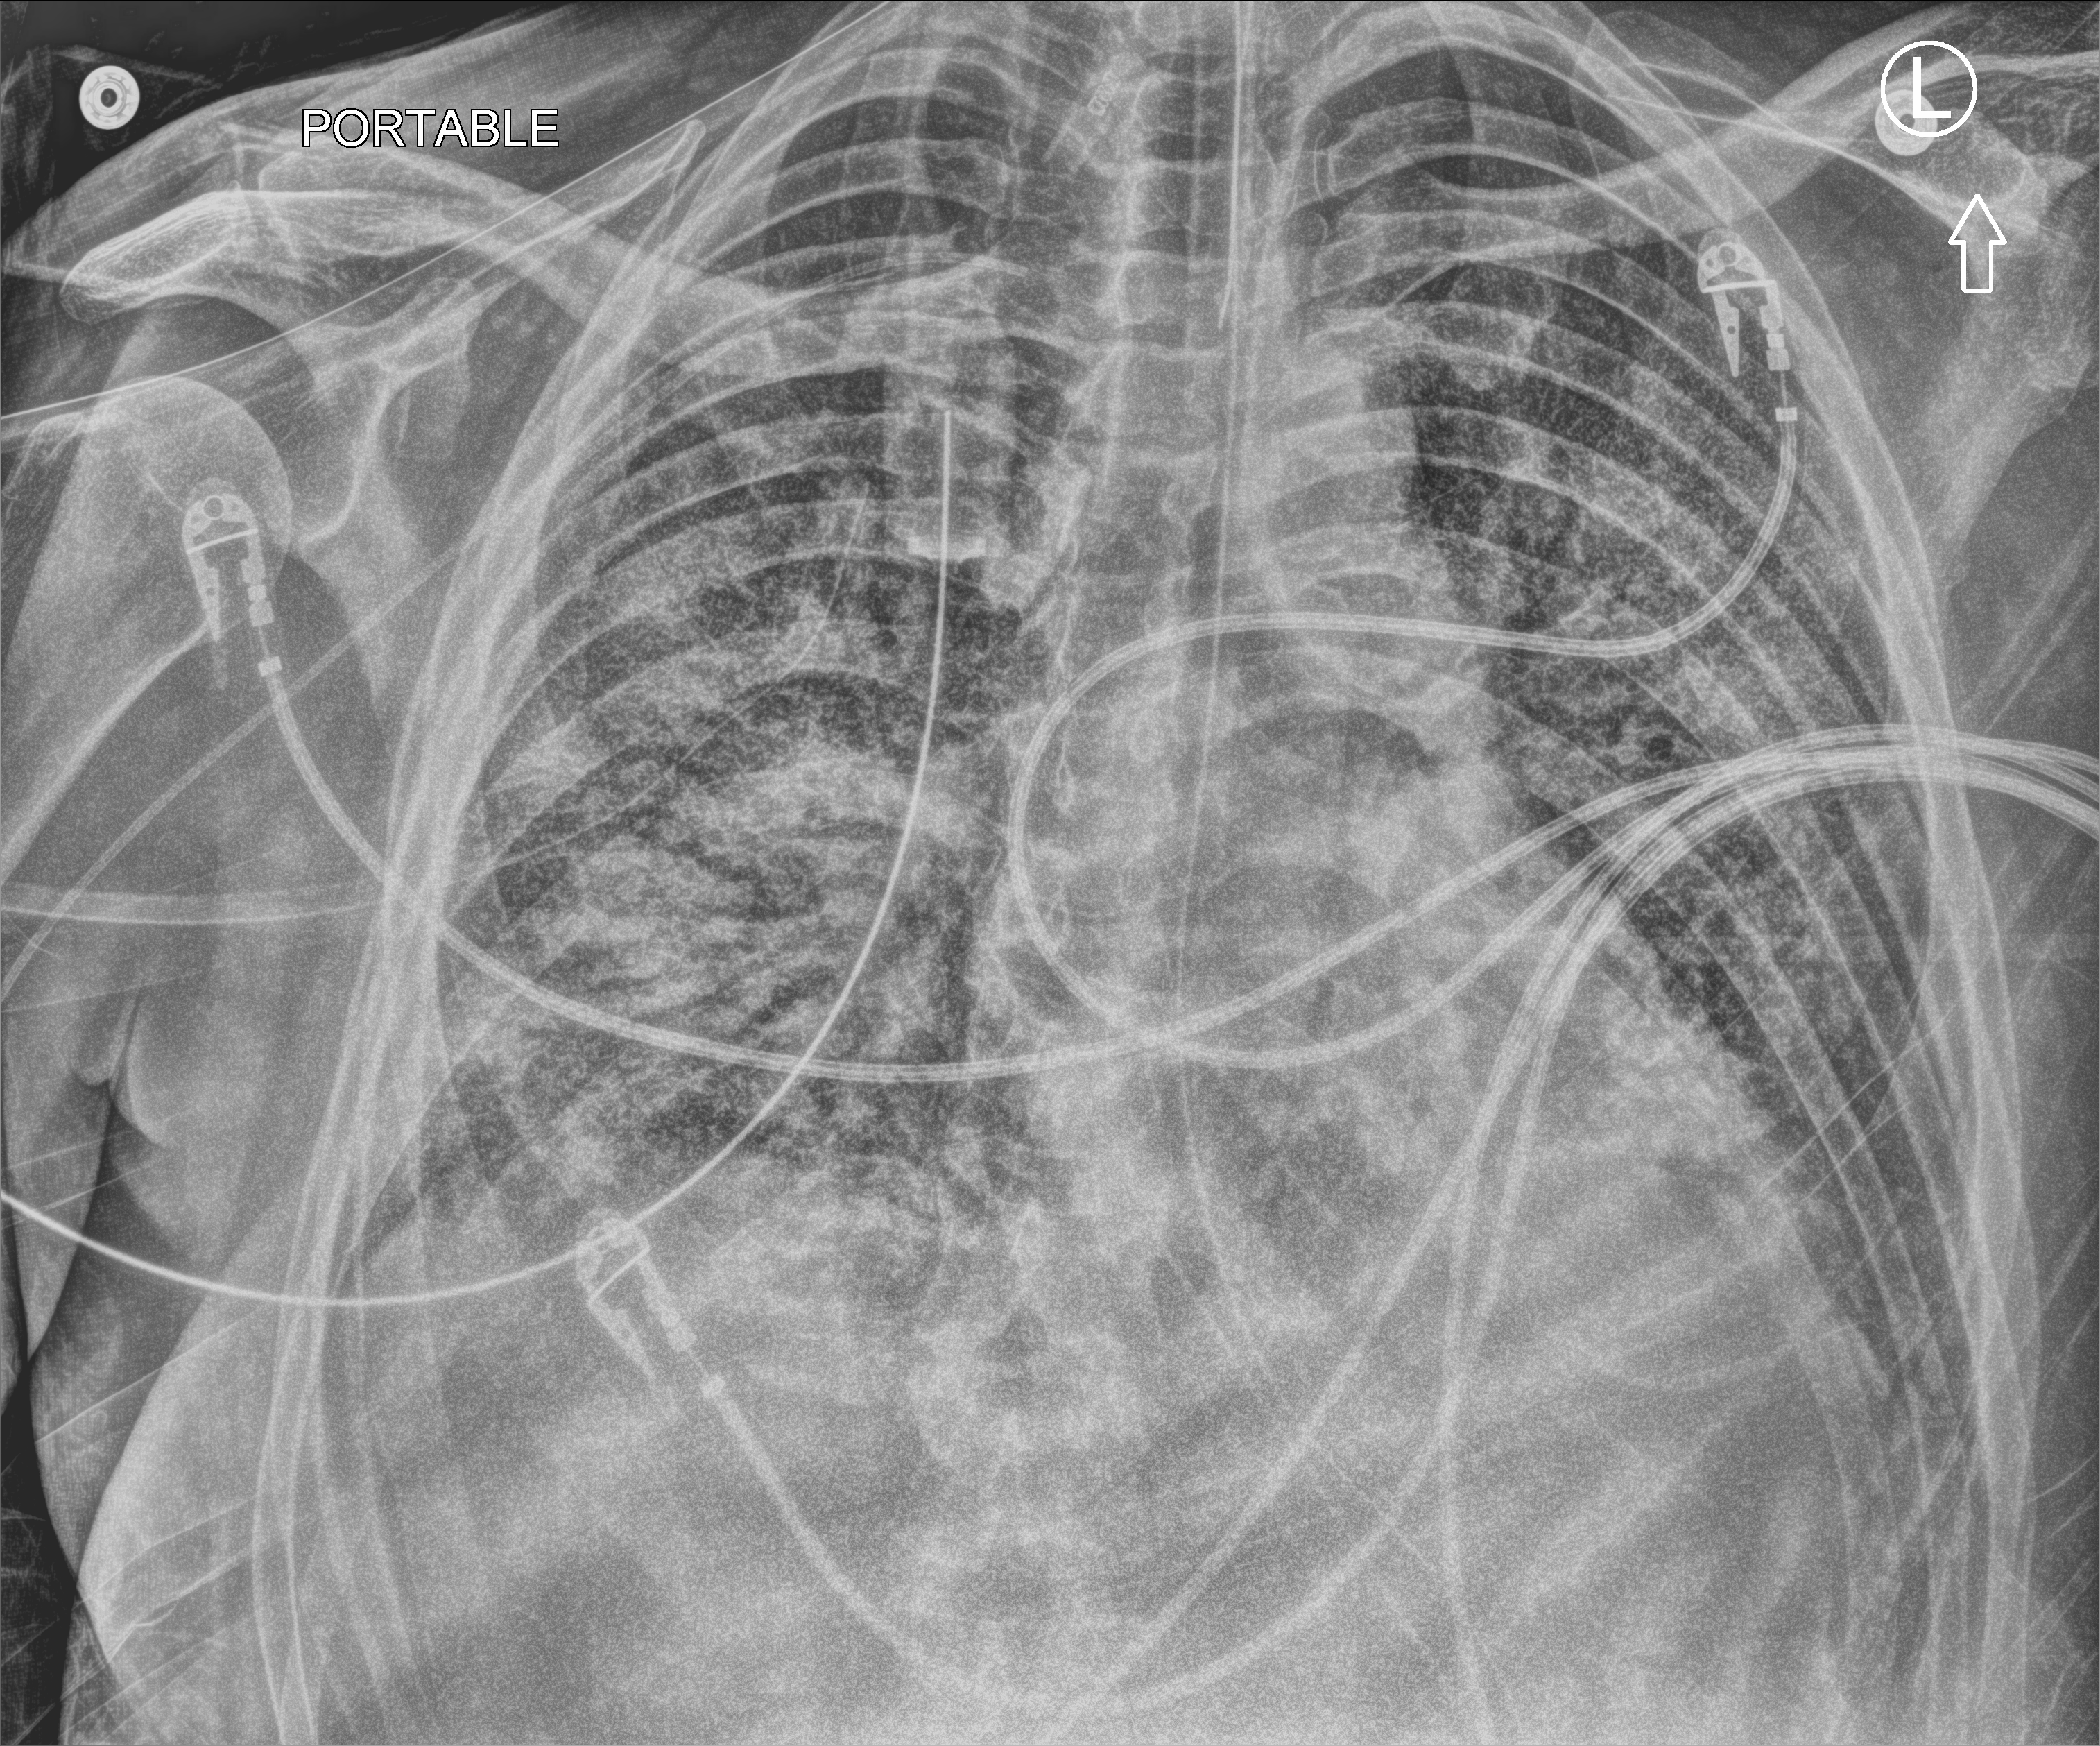
Chest X-ray (portable), anteroposterior (AP) projection. Male patient hospitalised with COVID-19, age 18–59 years.
From the hospital-stay record, not from the radiograph (when in the stay this image was taken is not recorded): admitted to intensive care during this hospital stay: yes.